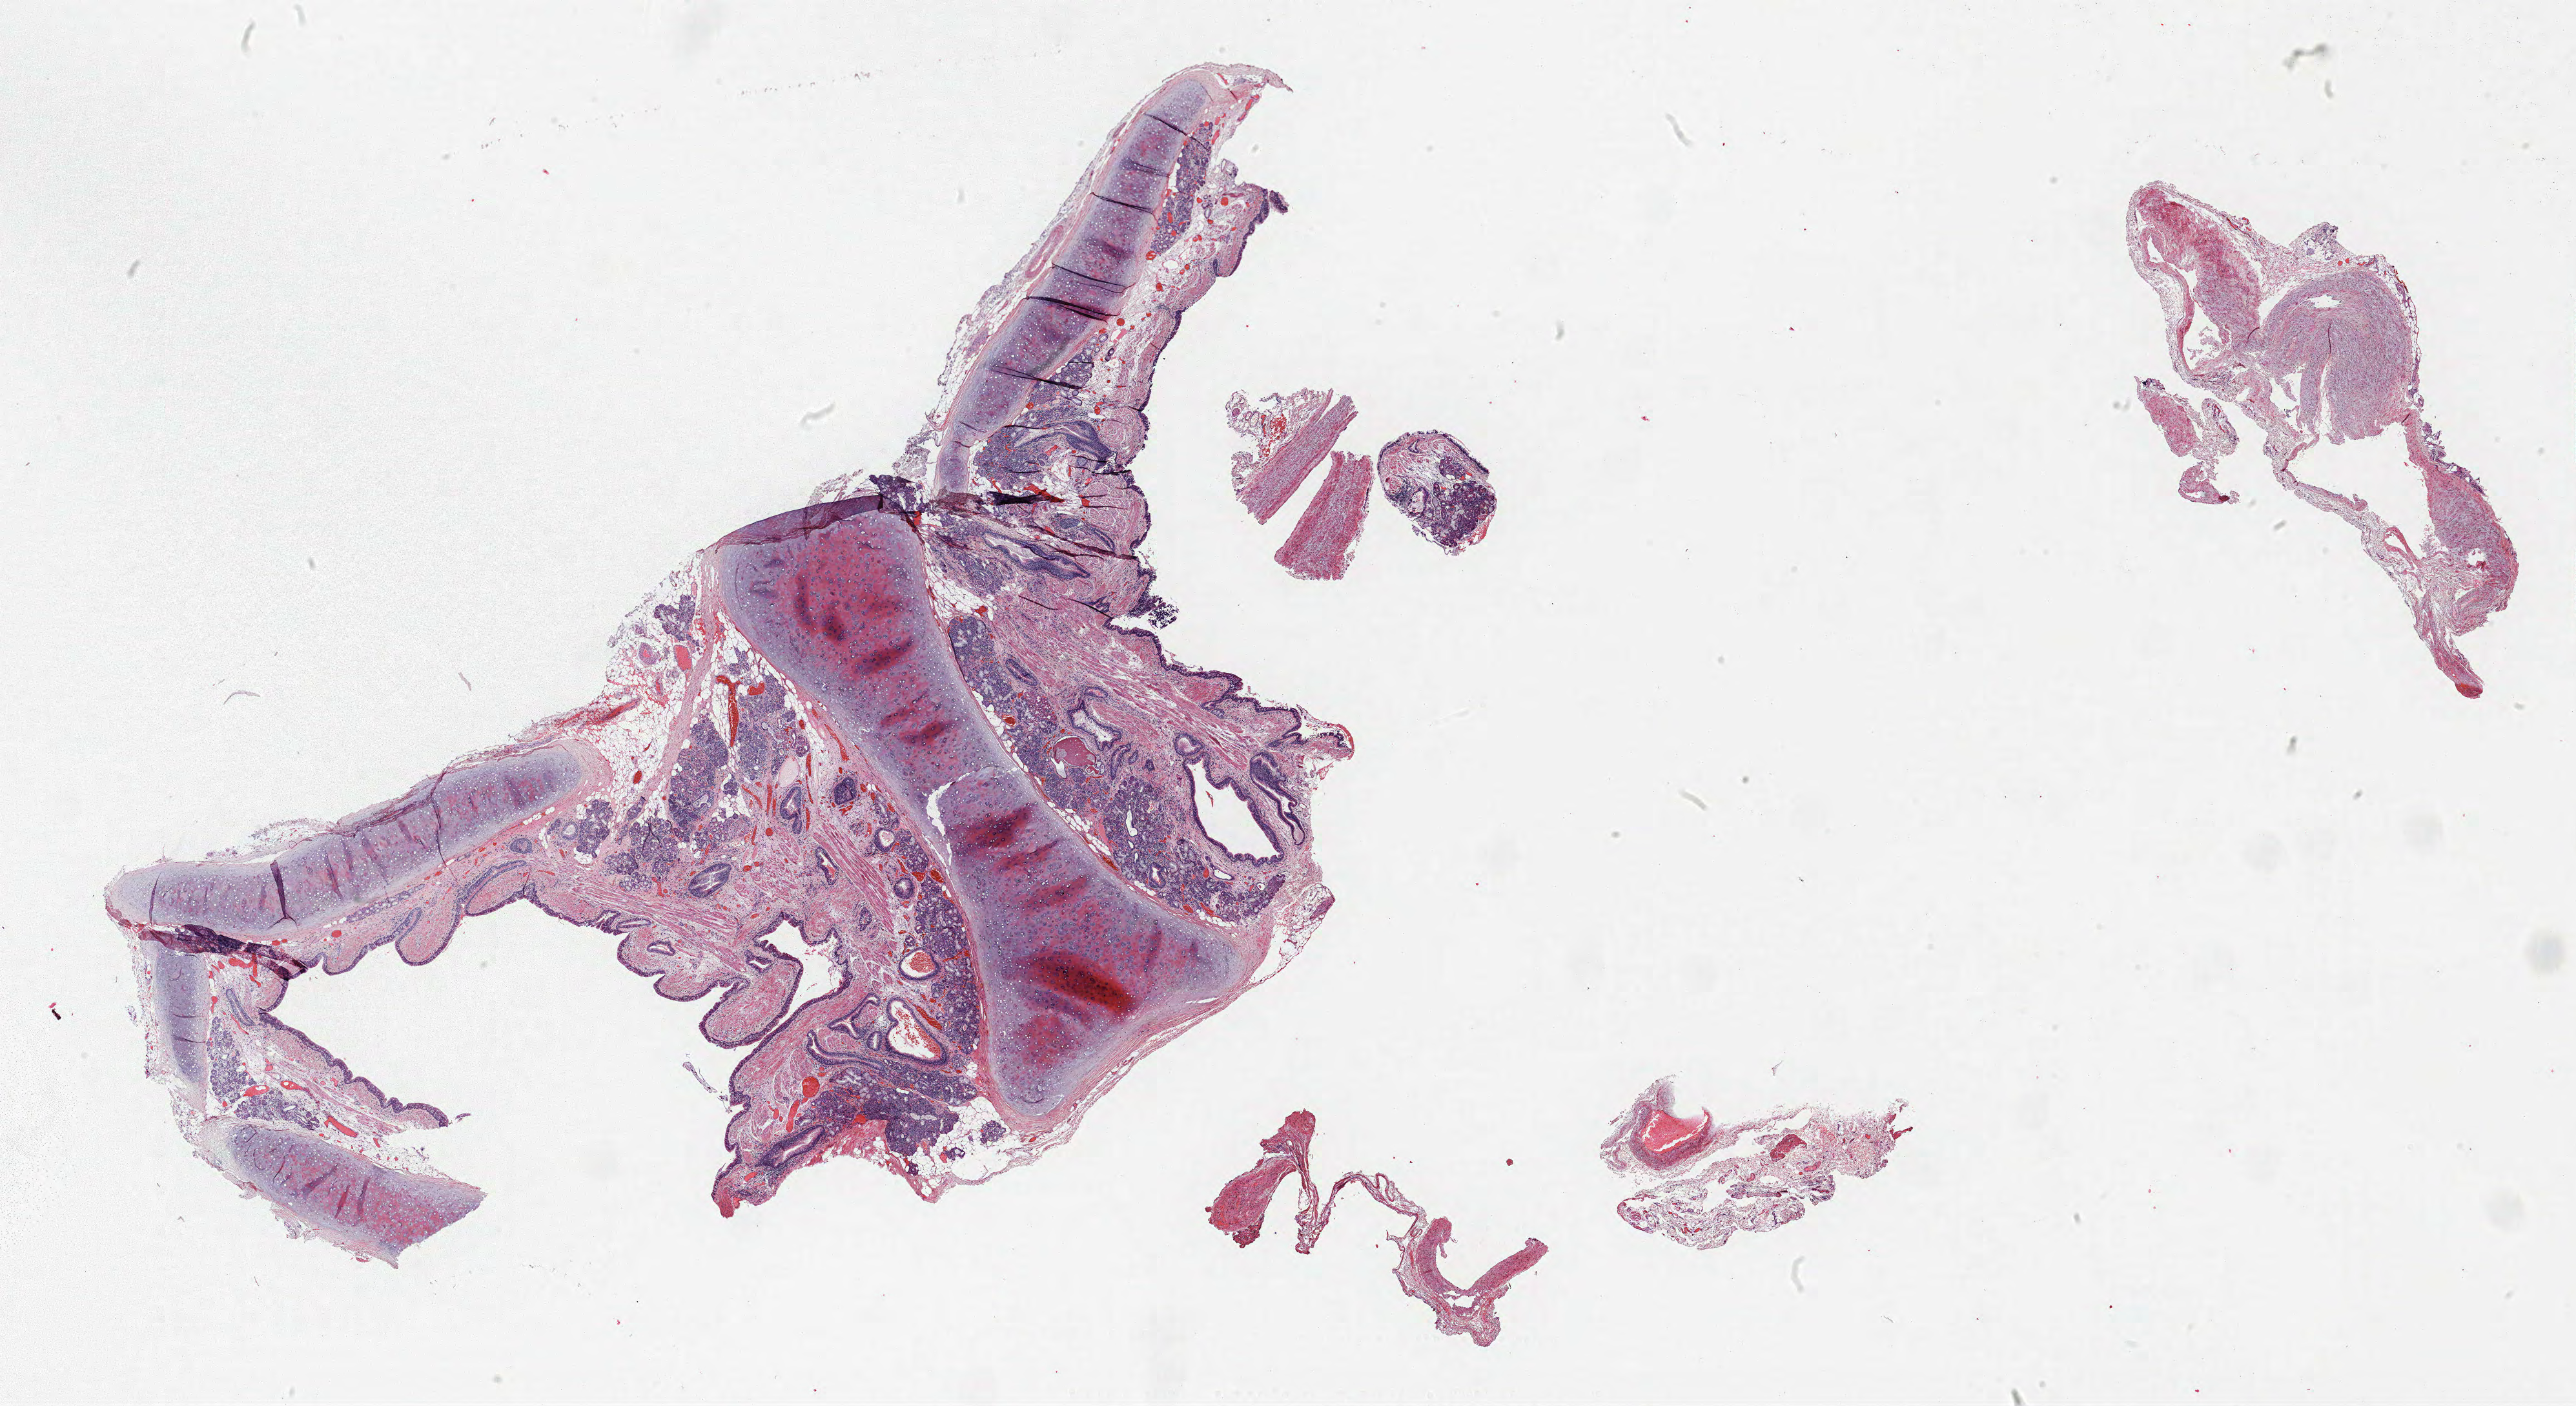
Whole-slide histology image, Hematoxylin and eosin (H&E) stained — a low-resolution overview of the entire scanned area, about 31.9 x 17.4 mm (from a 40x scan), FFPE section, lung. Male, age 68 at enrolment.
Participant's lung-cancer diagnosis: Squamous cell carcinoma, NOS (ICD-O-3 8070/3).